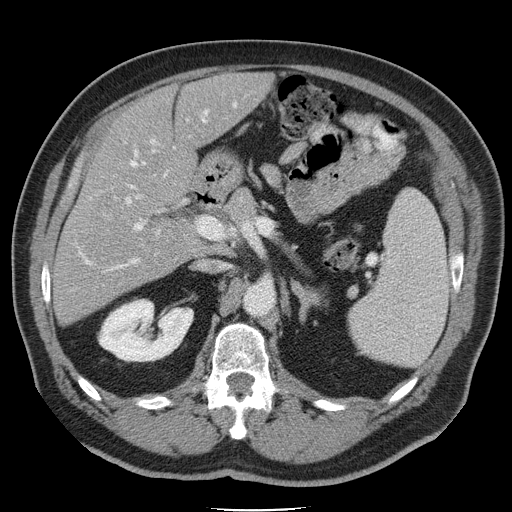
Contrast-enhanced abdominal CT, one axial slice; slice 24 of 45 in the series (ordered by position); intravenous contrast given; soft-tissue window (W 400 / L 40 HU); 5 mm slice thickness; 512 × 512 image matrix, field of view 386 × 386 mm. Male patient, age 65 years. From the clinical record (not read from this slice): diagnosis: colorectal cancer liver metastases, imaged before liver resection; multiple liver metastases: yes.
Outlined on this slice (outlined manually by an expert reader):
- hepatic veins: bounding box <78,102,237,272> (left, top, right, bottom; pixels)
- liver: <53,73,270,323>
- planned liver remnant (the part of the liver to remain after resection): <102,73,269,201>
- portal vein (with intrahepatic branches): <104,139,163,237>